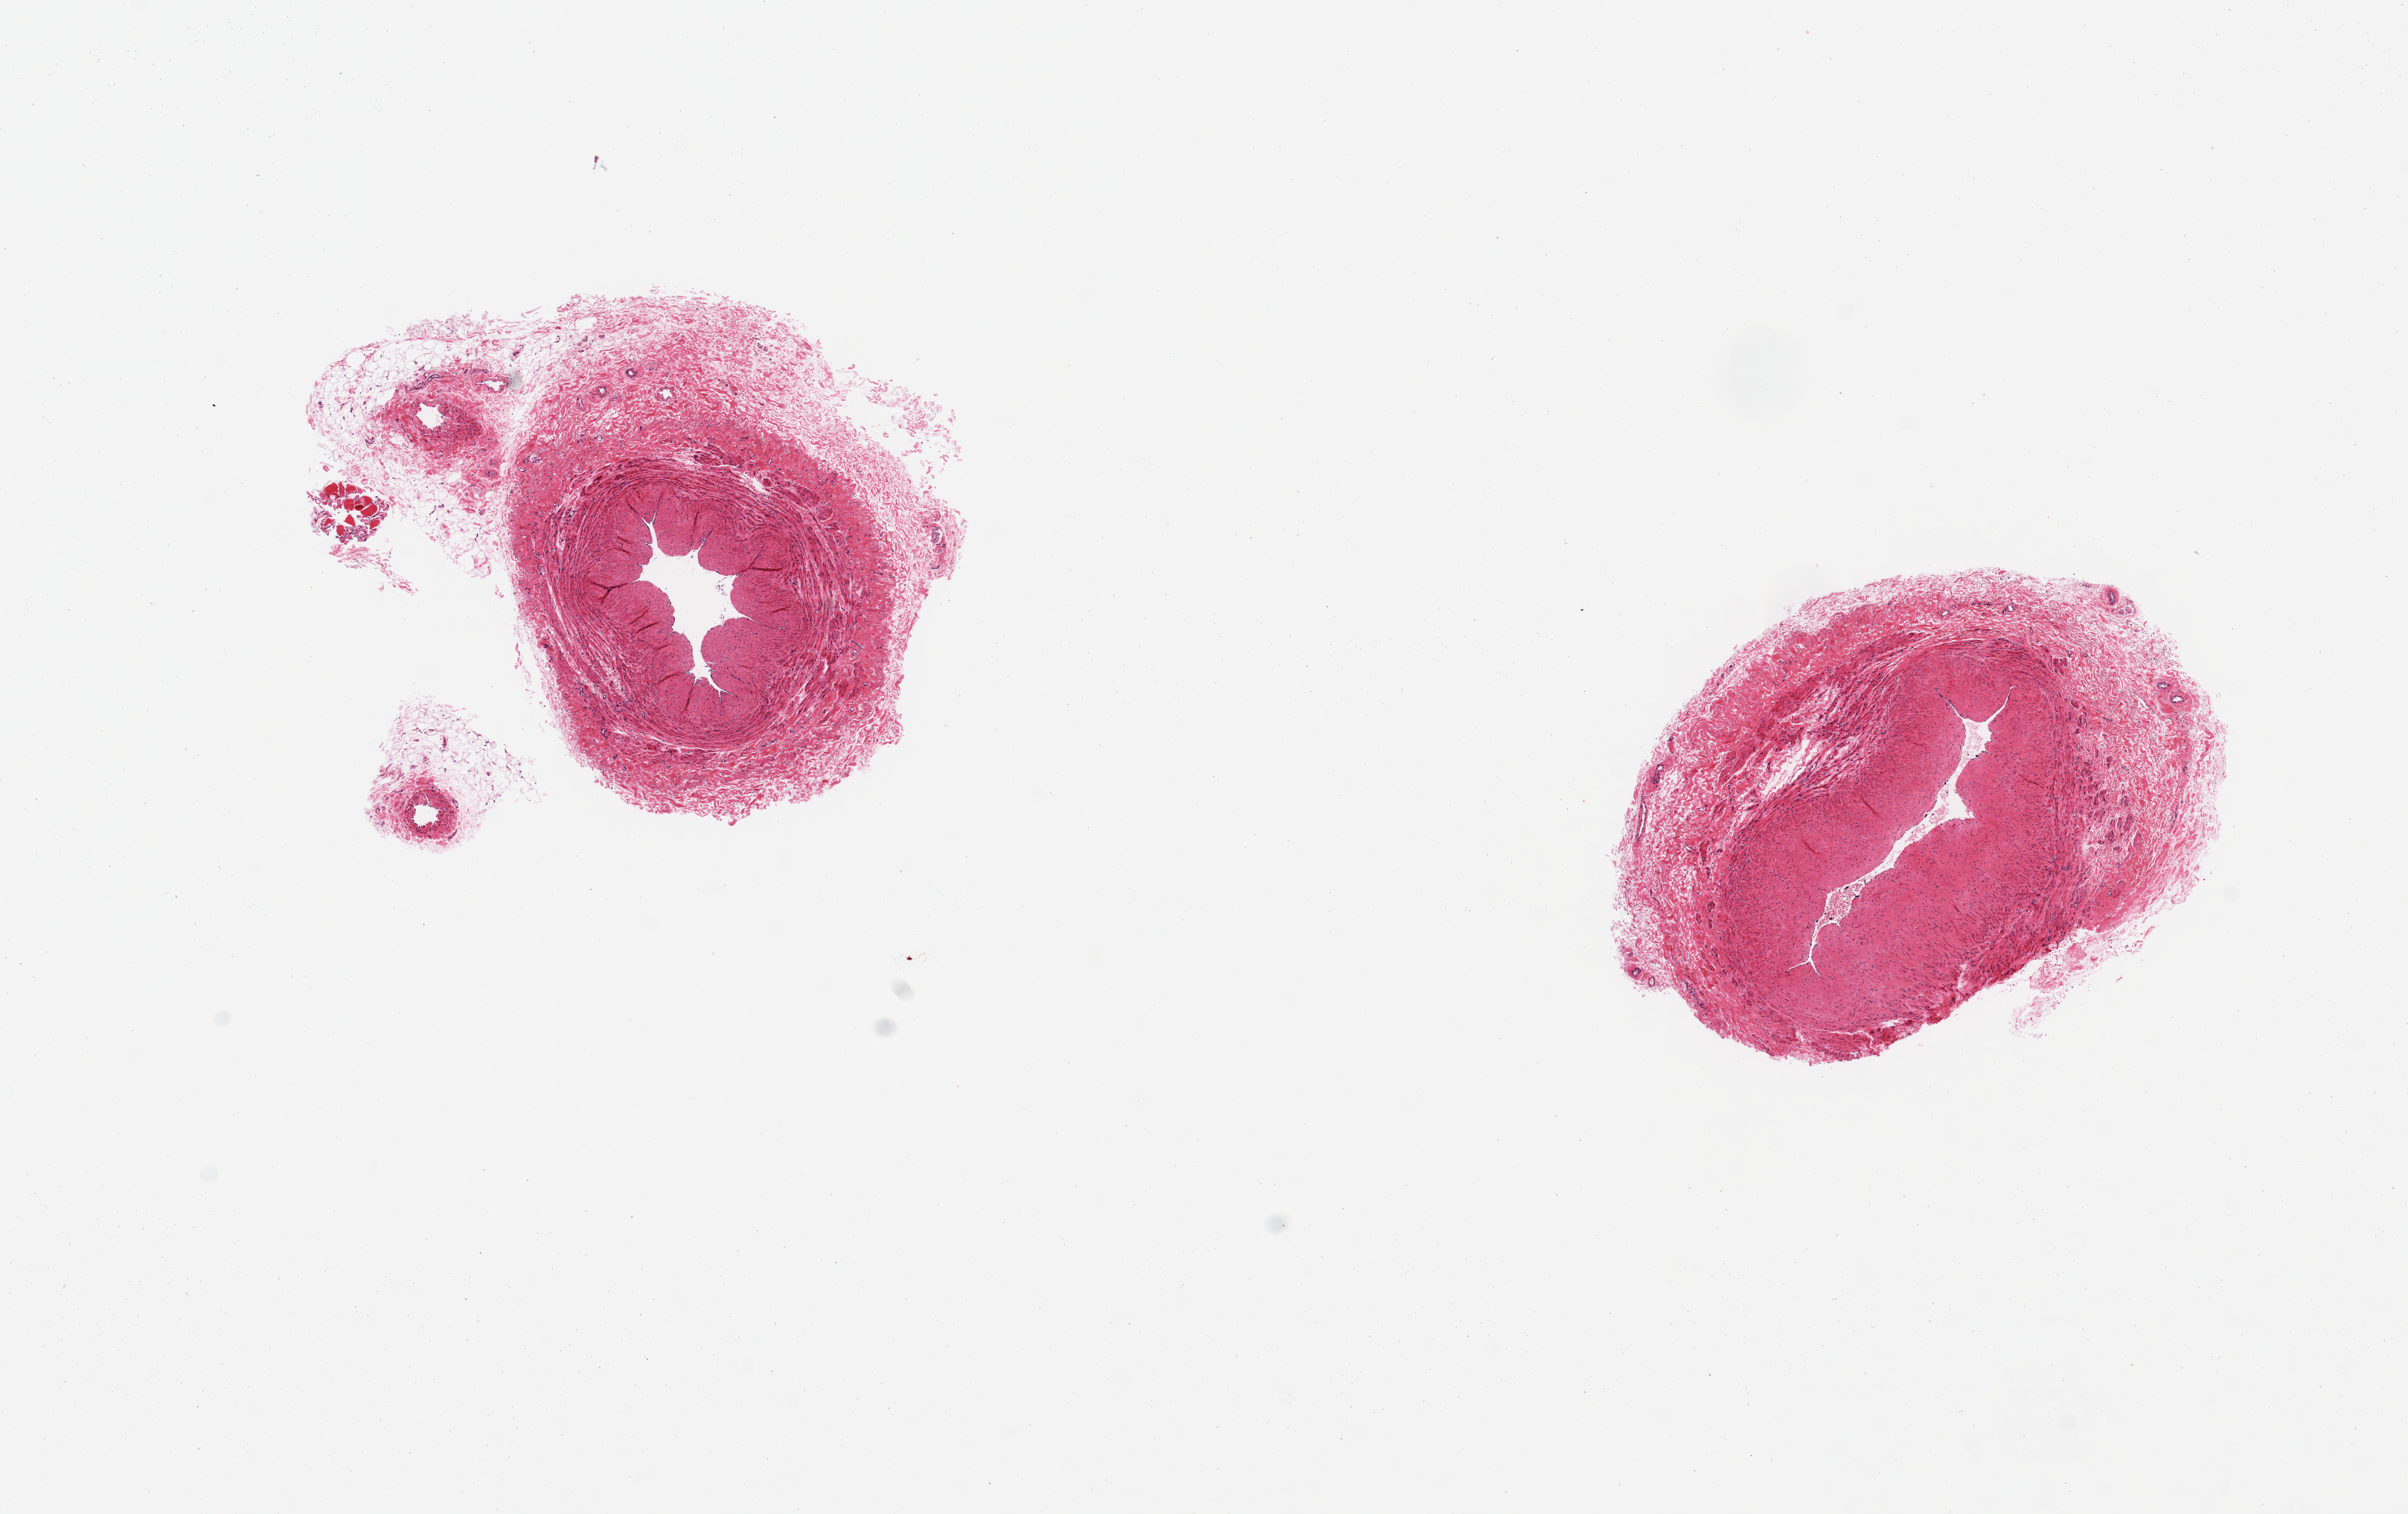
Digitized haematoxylin and eosin-stained section — whole scanned area (about 12.8 x 8.0 mm) shown as a low-resolution overview, PAXgene-fixed paraffin-embedded (PFPE) section, target tissue: tibial artery, donor tissue sample. Donor: female.
Review note (as recorded): 2 pieces rim of adherent fat/fibrous tissue up to ~0.8mm, ~40% total tissue; sample with care.